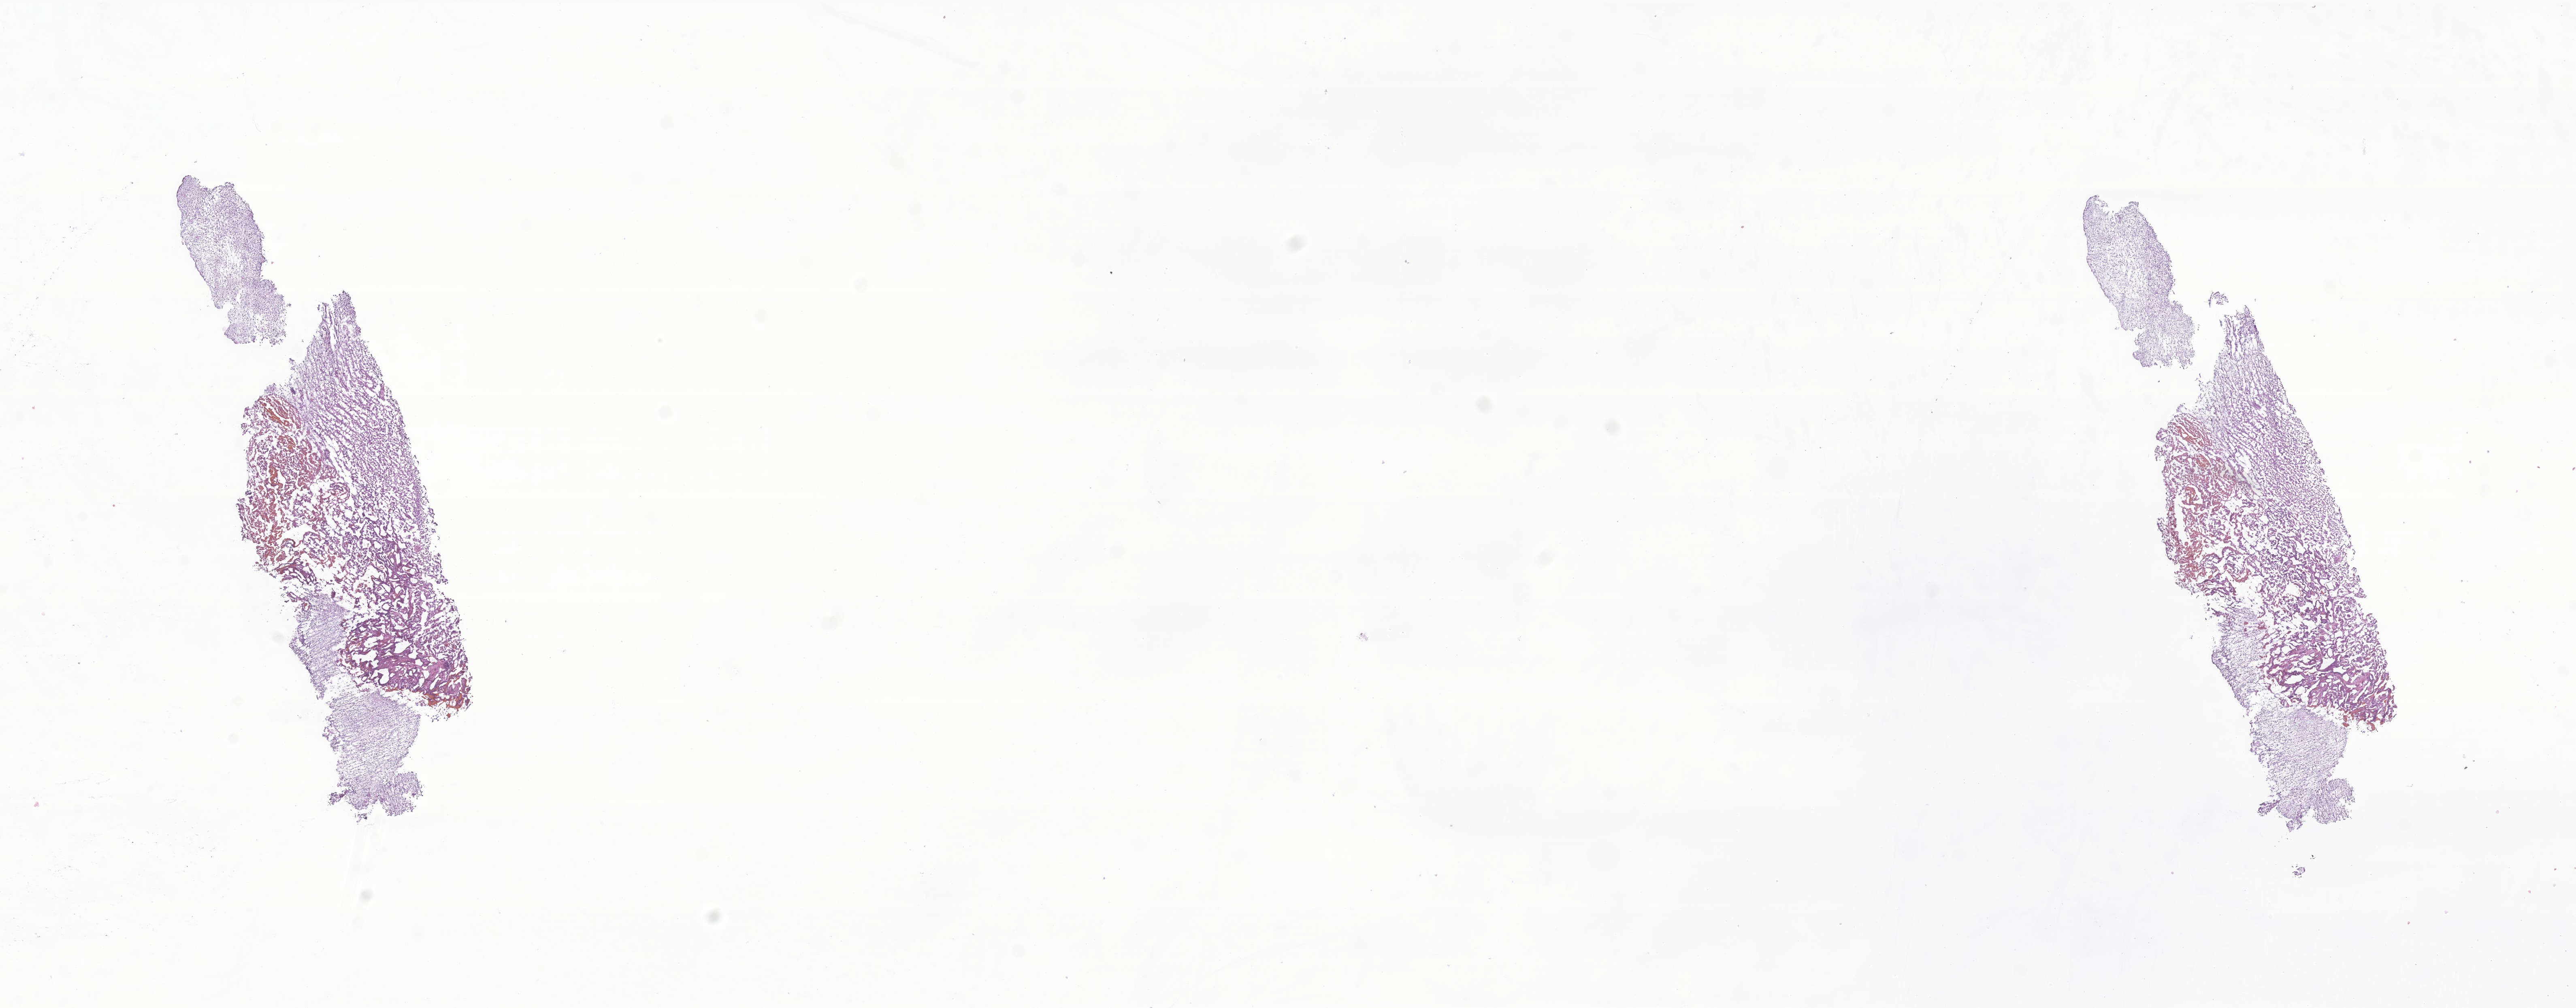
Digitized H&E-stained section of tumor tissue from the central nervous system, shown as a low-resolution overview of the whole scanned area (about 26.8 x 10.5 mm). Frozen section (OCT-embedded). Patient male; age 89 months (7 years 5 months).
Recorded diagnosis: Medulloblastoma, NOS.